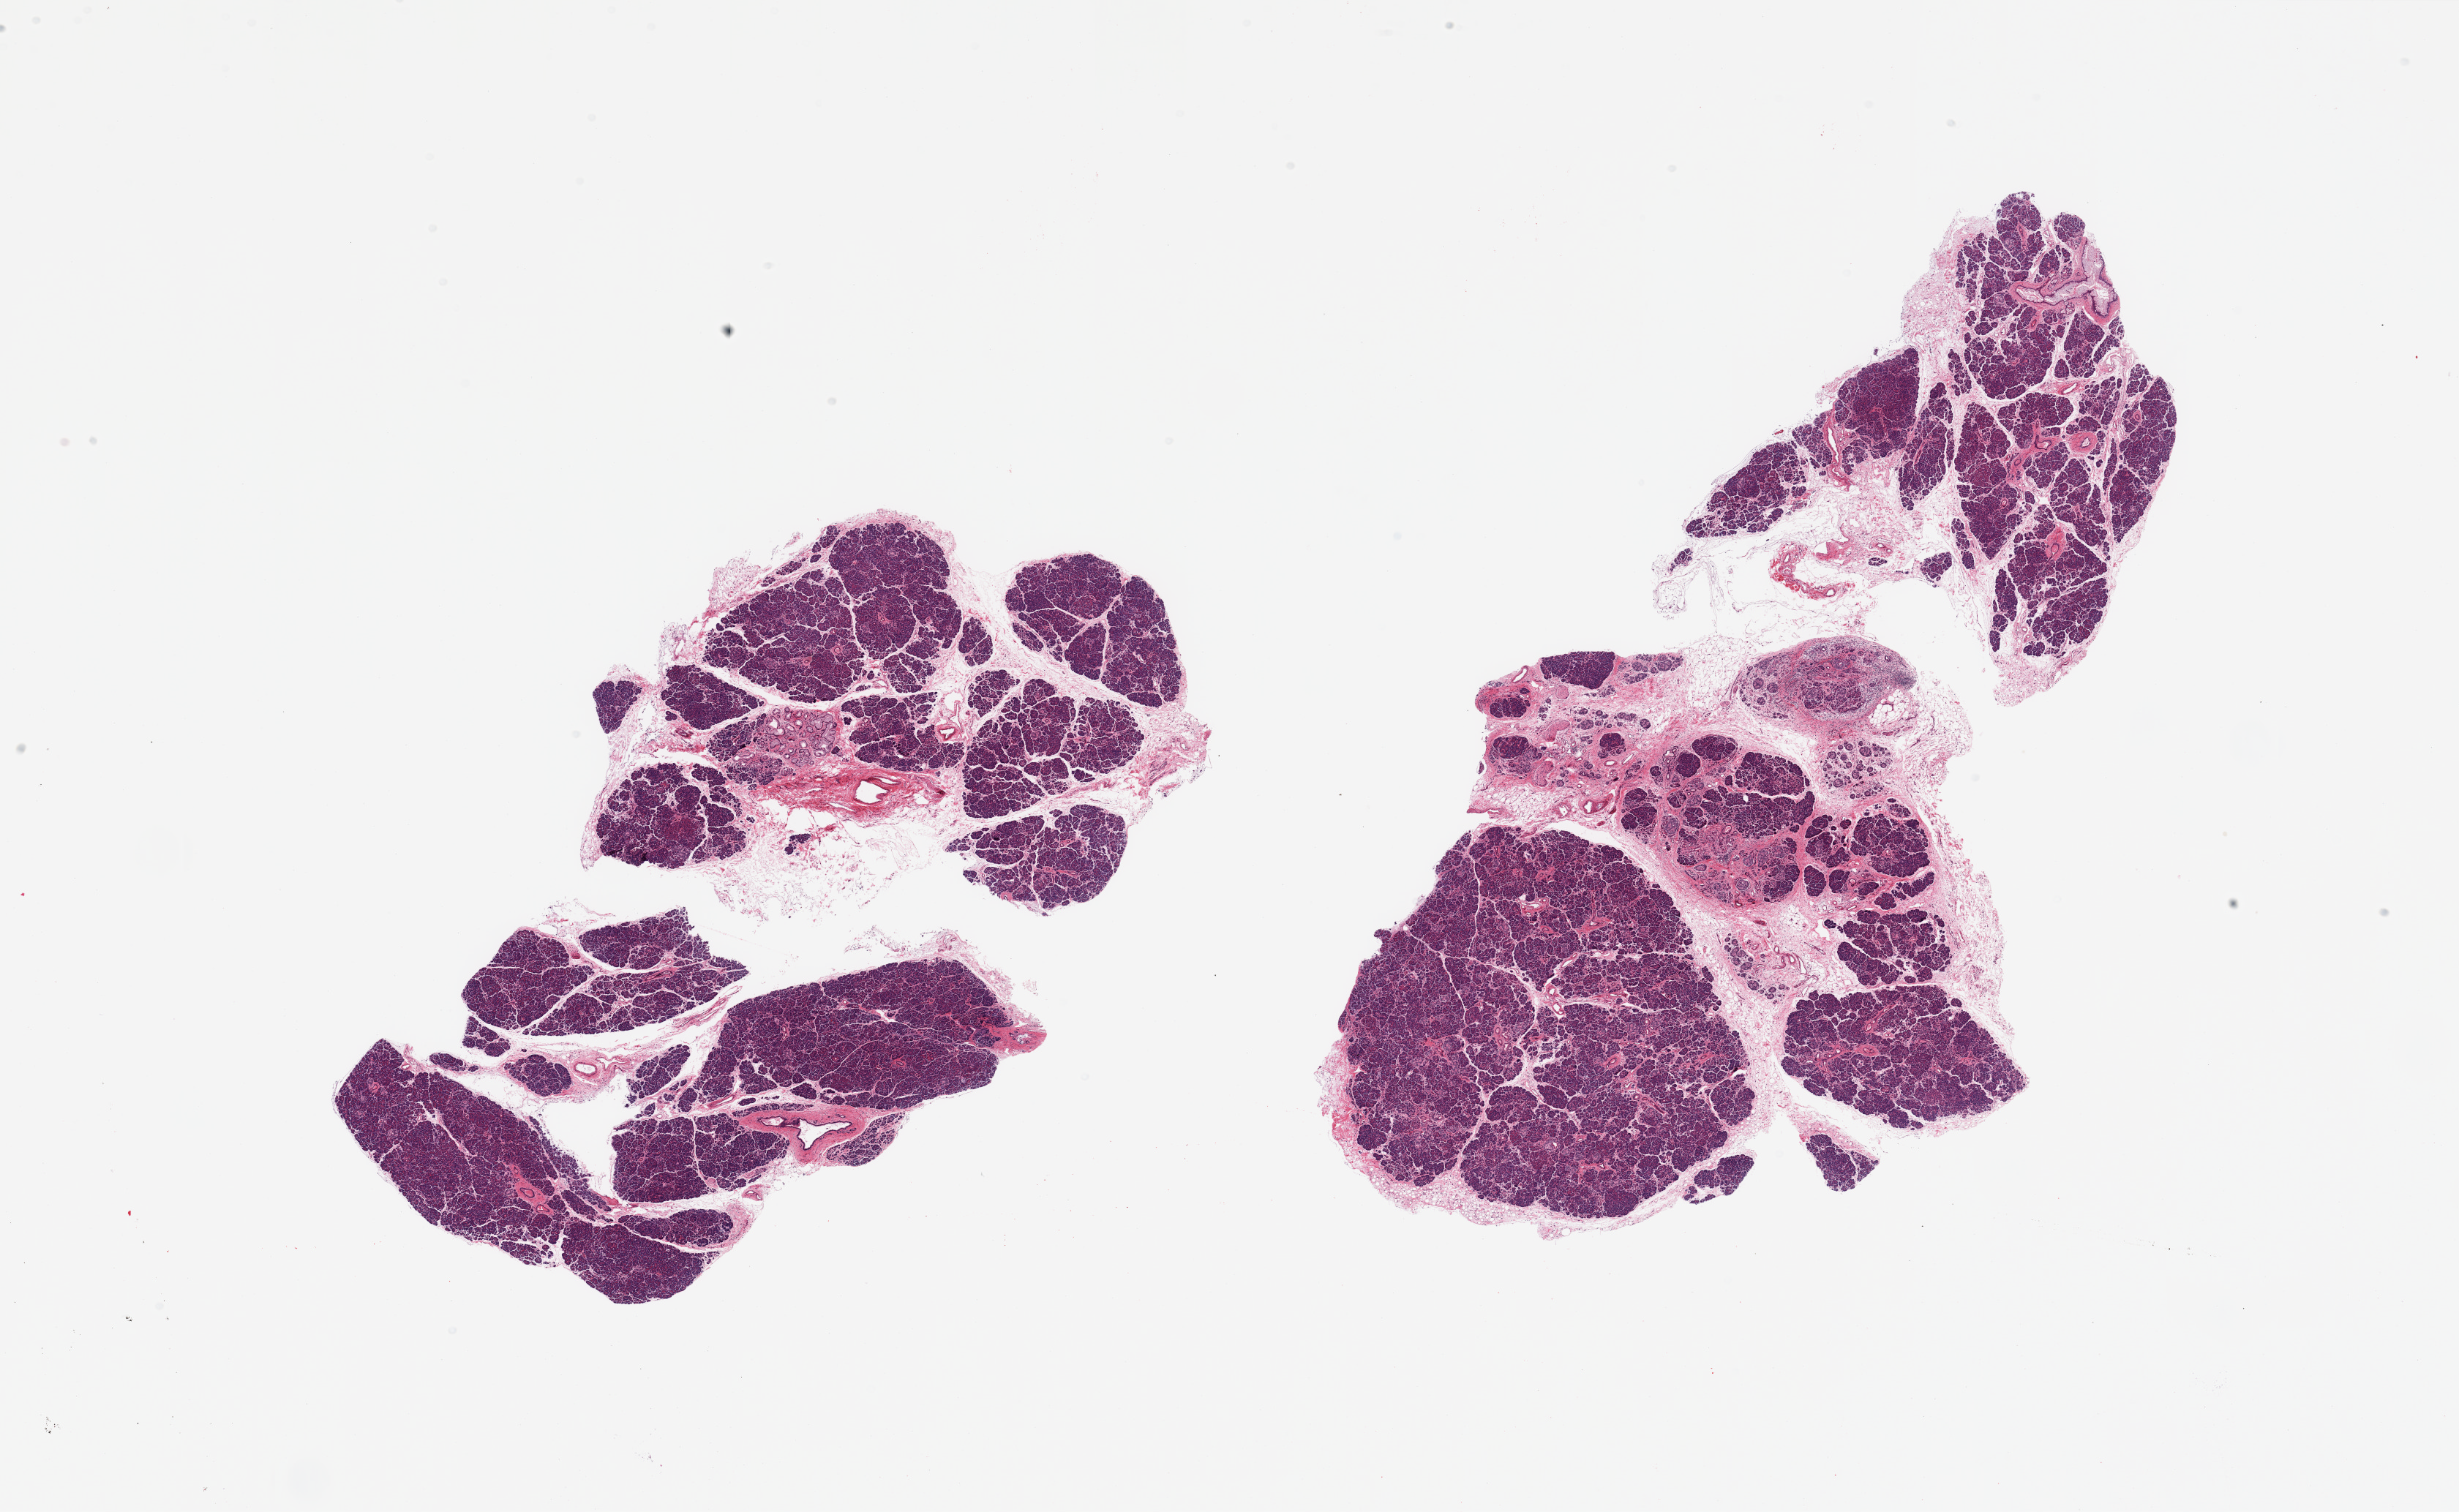
Whole-slide image, H&E stain, brightfield, a low-resolution overview of the entire scanned area, about 26.6 x 16.3 mm. PAXgene-fixed paraffin-embedded (PFPE) section. Target tissue: pancreas. Donor tissue sample. Donor sex: male.
Review note (as recorded): 2 pieces; some atrophy and chronic inflammation present with focal PanIN1.